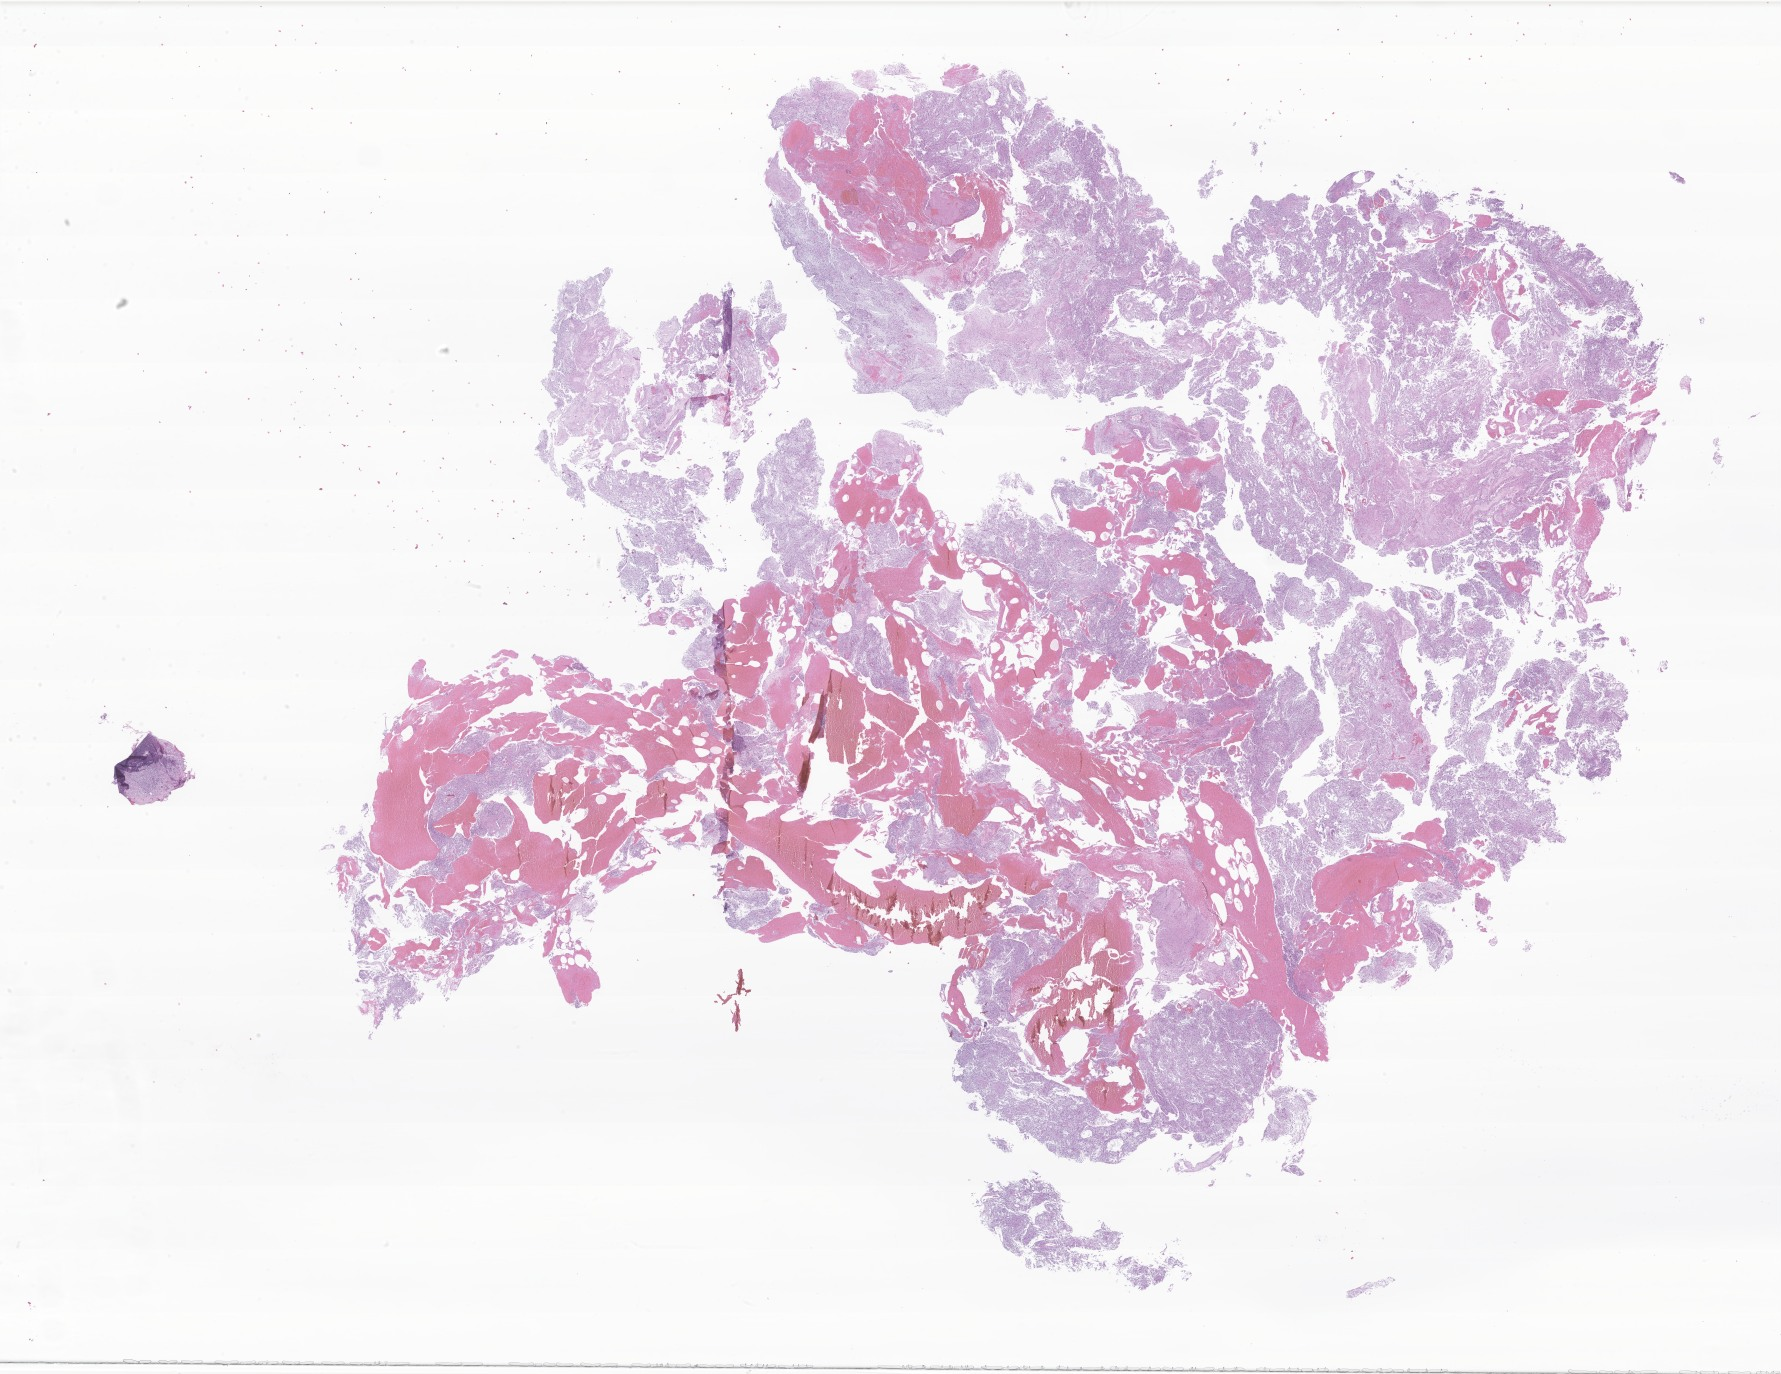
Whole-slide image, haematoxylin and eosin stain of tumor tissue from the brain — shown as a low-resolution overview of the whole scanned area (about 30.0 x 23.2 mm); formalin-fixed, paraffin-embedded (FFPE) tissue. Patient female; age 189 months (15 years 9 months).
Diagnosis (ICD-O-3 morphology term): Pilocytic astrocytoma.